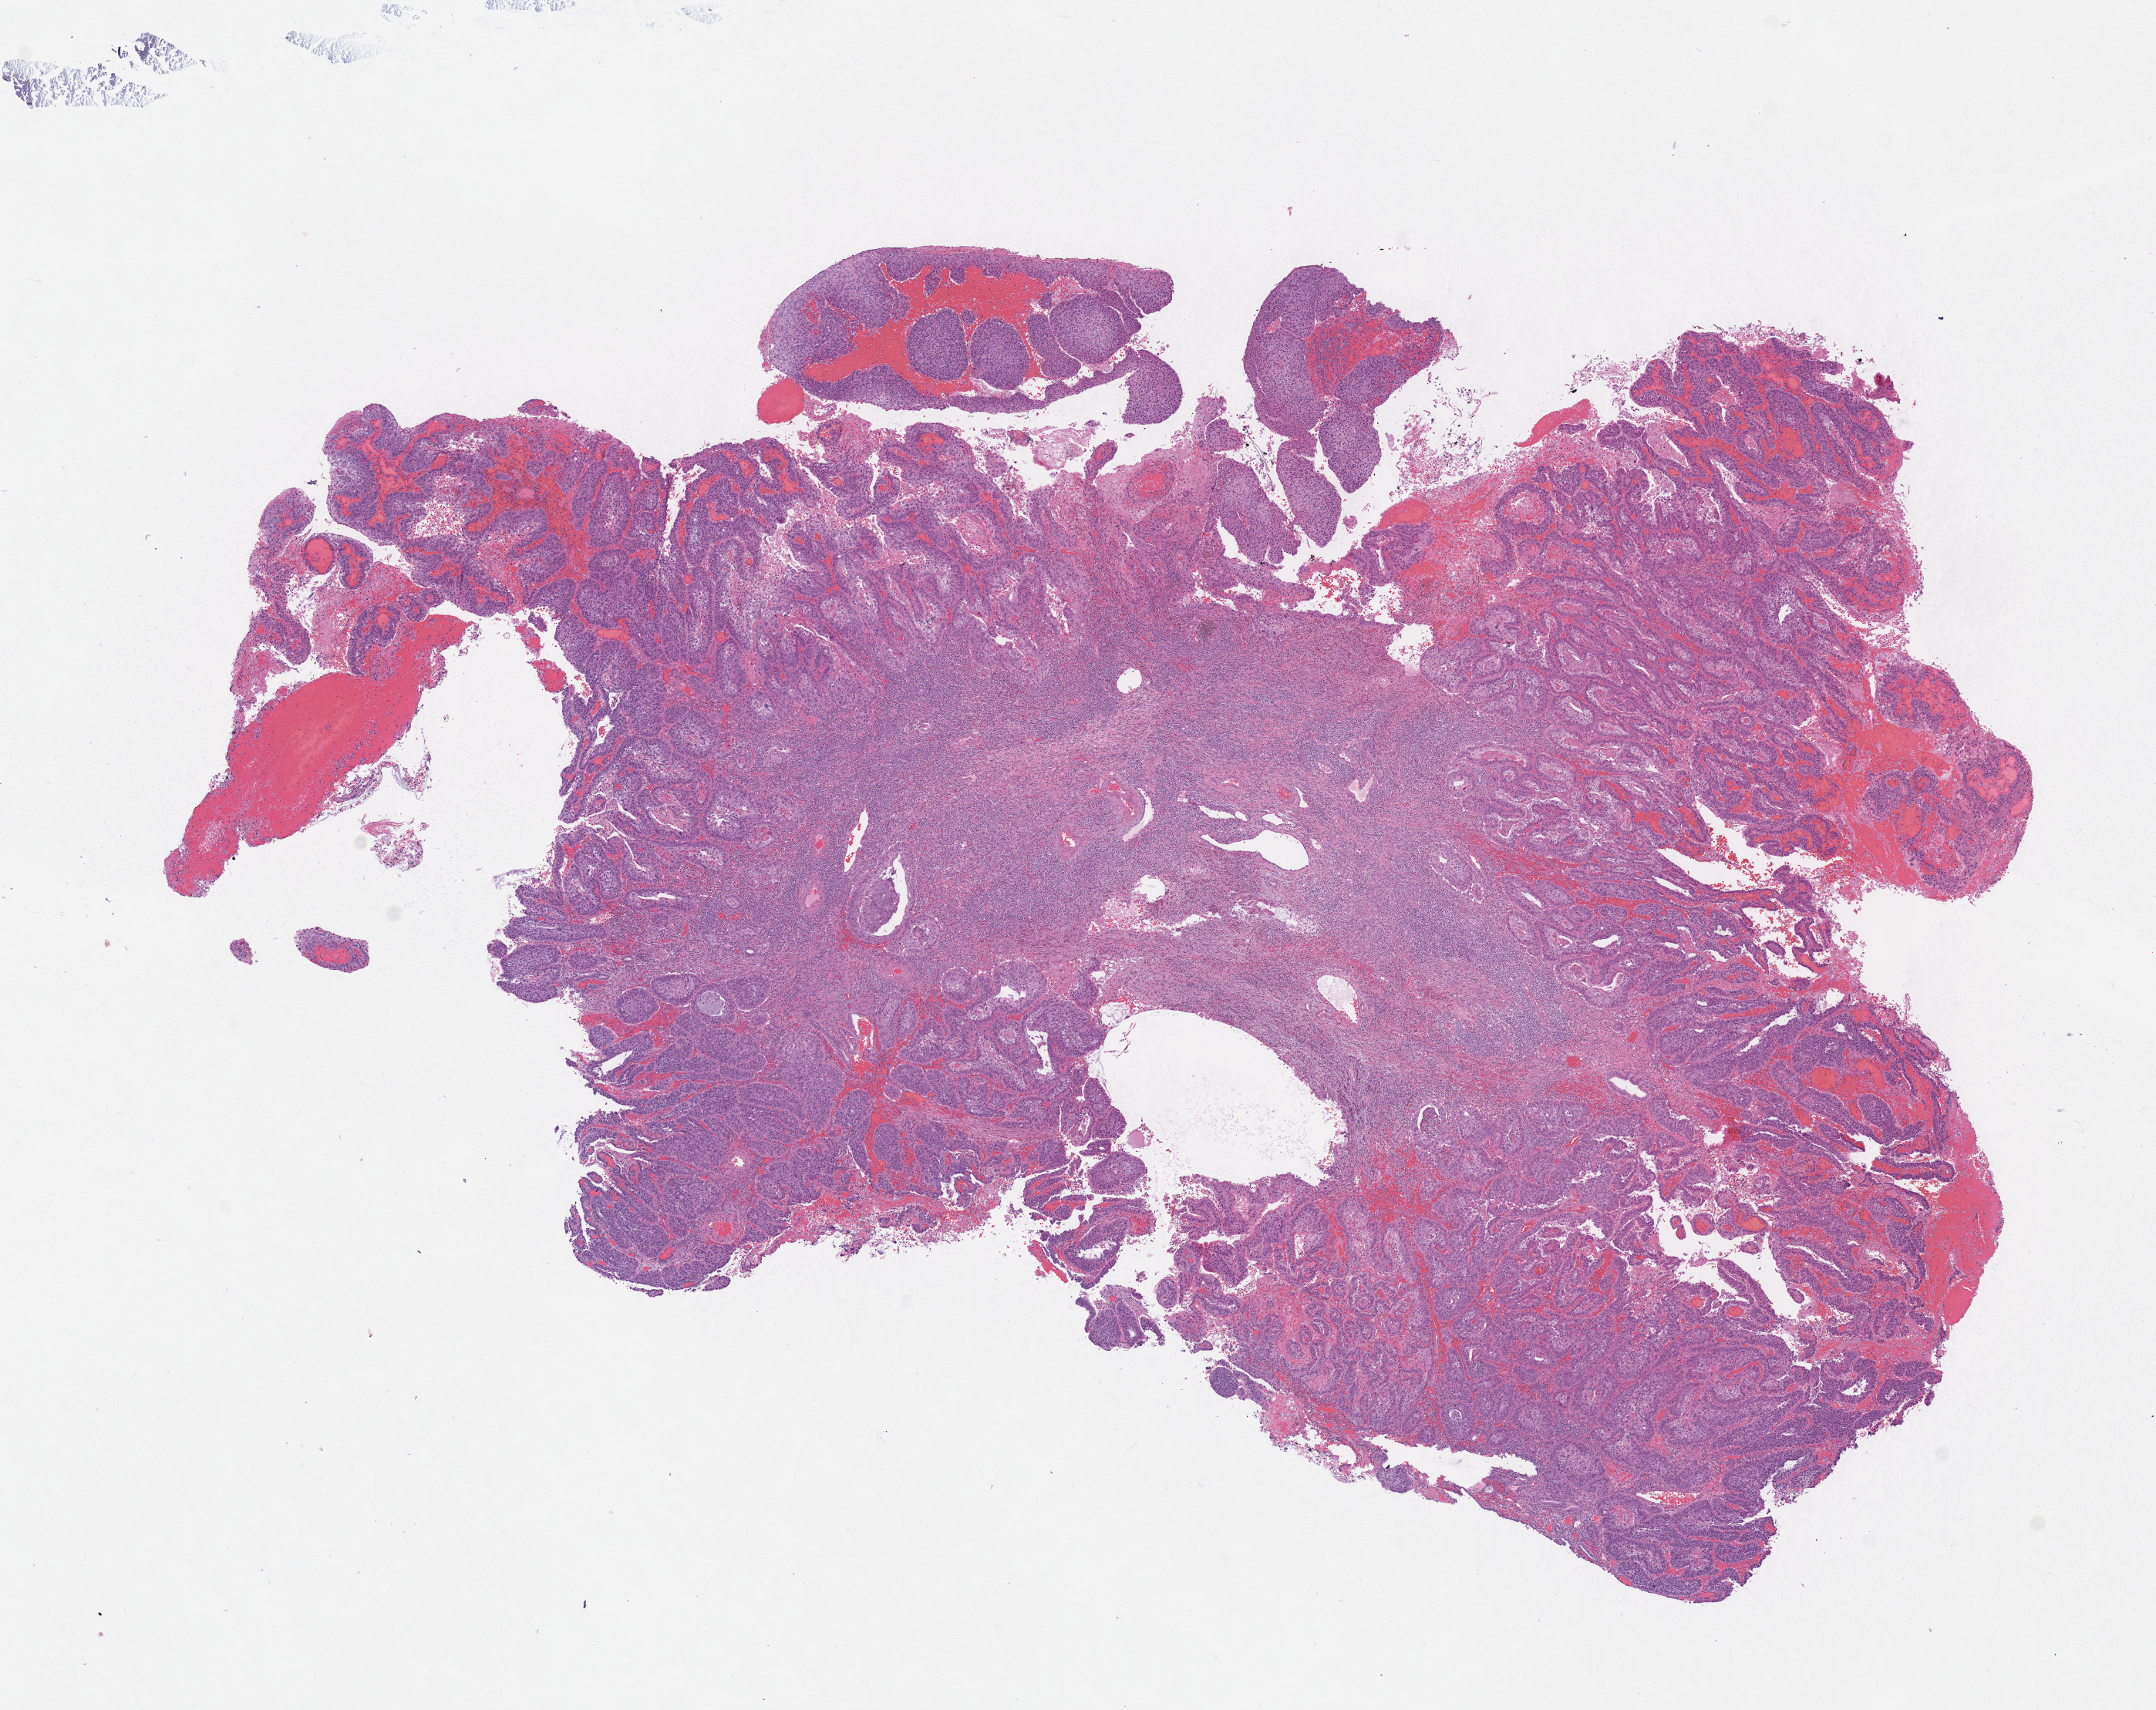
Whole-slide histology image, H&E — low-resolution overview of the scanned area, about 11.0 x 8.7 mm (slide scanned at 40x), FFPE section, cervix, primary tumour sample. Patient: female, age at initial diagnosis 29 years.
Histologic diagnosis: Squamous cell carcinoma, keratinizing, NOS (cervix uteri).